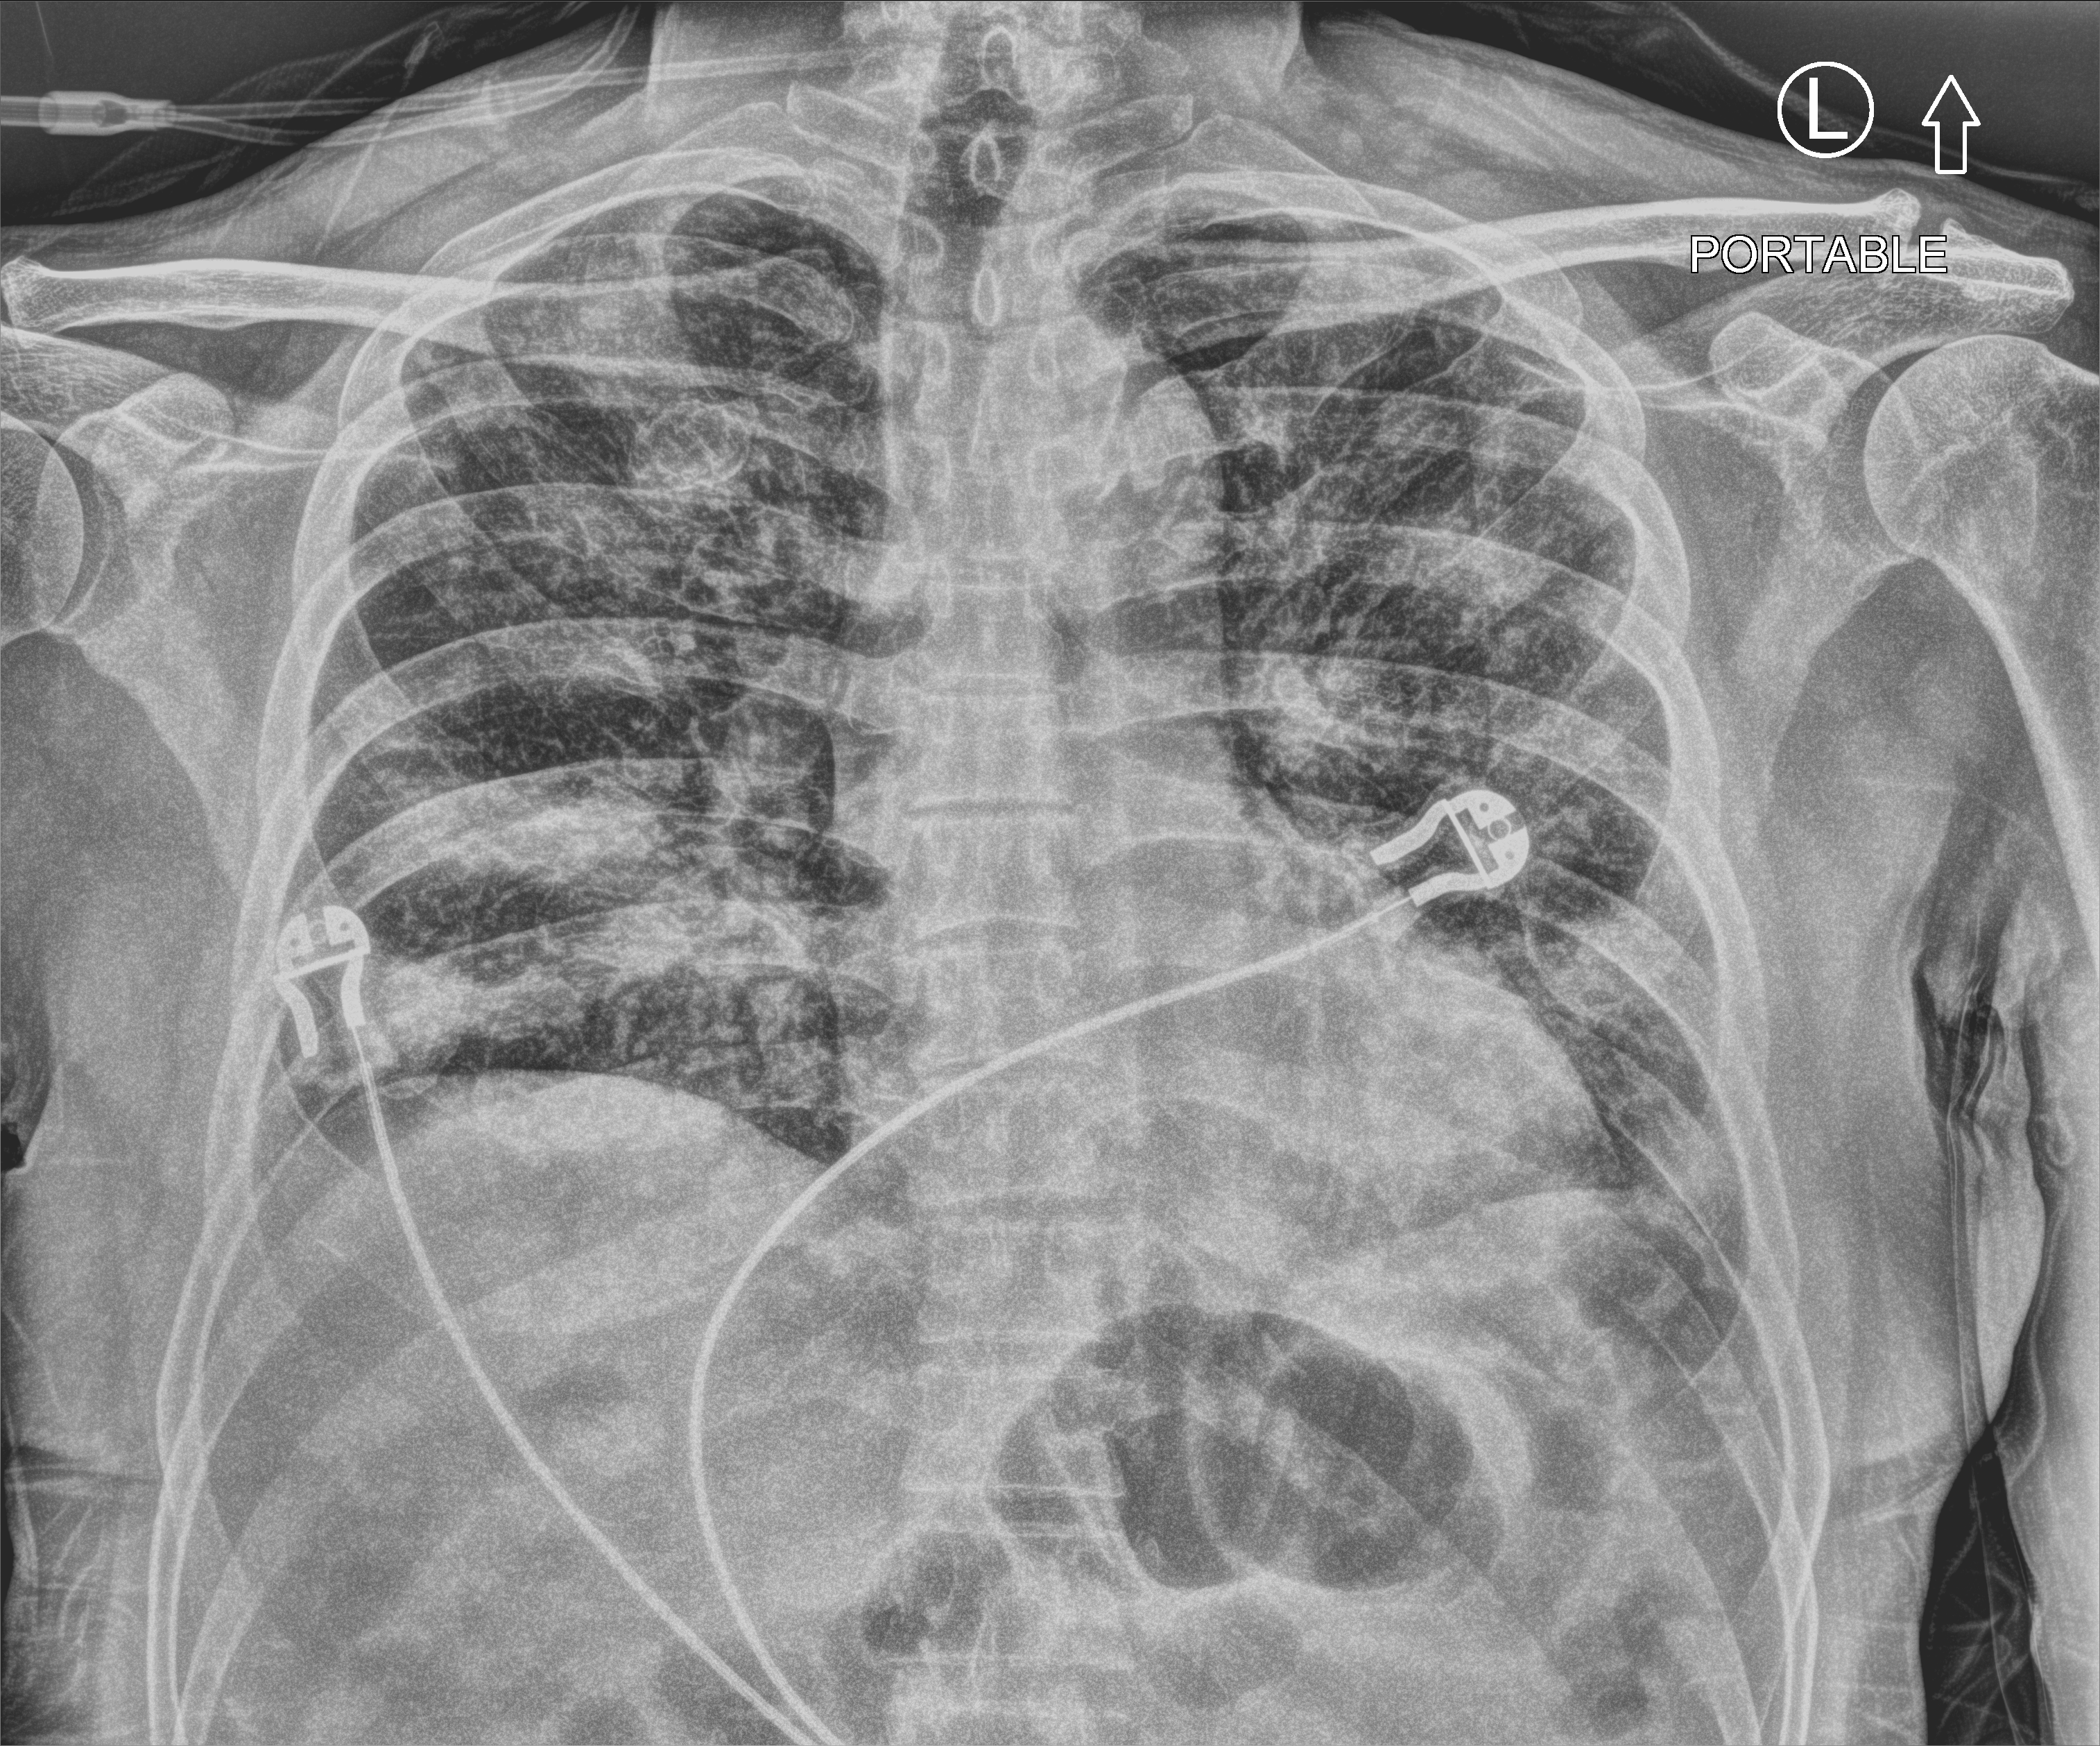
Bedside chest radiograph (computed radiography); anteroposterior (AP) projection. Patient hospitalised with COVID-19; male, aged 60–74 years.
From the hospital-stay record, not from the radiograph (when in the stay this image was taken is not recorded):
- length of hospital stay: 31 days